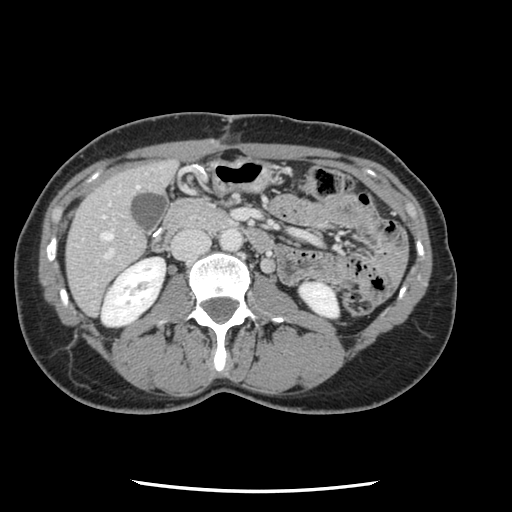
Contrast-enhanced abdominal CT, one axial slice. Position 33 of 134 along the scan axis. 120 kVp. Intravenous contrast given. Soft-tissue window (W 400 / L 40 HU). 2.5 mm slice thickness. 512 × 512 image matrix, field of view 330 × 330 mm. Female patient, age 43 years. From the clinical record (not read from this slice): diagnosis: colorectal cancer liver metastases, imaged before liver resection; multiple liver metastases: yes; largest metastasis: 3.4 cm.
Annotated regions visible in this slice (outlined manually by an expert reader):
- hepatic veins: bounding box [x1, y1, x2, y2] px = [102, 232, 112, 240]
- liver: [67, 161, 176, 315]
- planned liver remnant (the part of the liver to remain after resection): [67, 161, 177, 315]